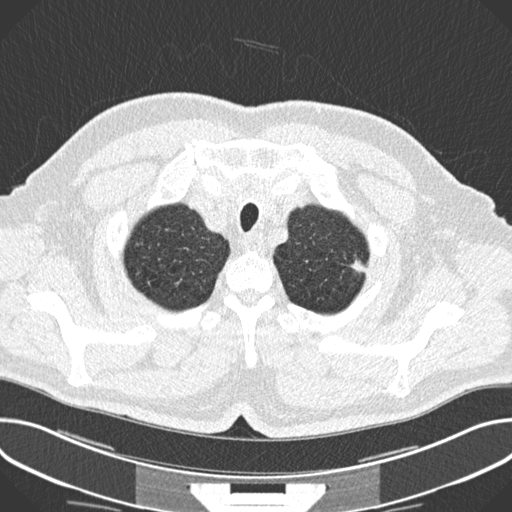
Low-dose screening chest CT, one axial slice; position 219 of 244 along the scan axis; 120 kVp; lung window (W 1500 / L -600 HU); 512 × 512 image matrix.
Annotated regions visible in this slice (manually delineated by an expert):
- lesion 1 (tumor, upper lobe of left lung): bounding box <350,259,368,276> (left, top, right, bottom; pixels)